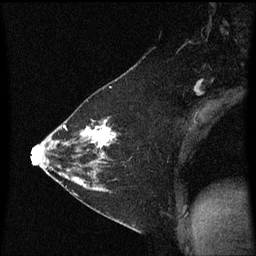
Breast MRI (dynamic contrast-enhanced), one sagittal slice; position 38 of 60 along the scan axis; dynamic contrast-enhanced series, image 2 of 3 at this slice position (ordered by acquisition); 1.5 T; TE 4.2 ms, TR 8.4 ms; 2 mm slice thickness; 256 × 256 image matrix, field of view 200 × 200 mm. Female patient, age 36 years. Case-level facts recorded for this patient, not image findings: setting: breast cancer imaged before/during neoadjuvant chemotherapy; receptor status: HR-positive, HER2-negative.
Outlined on this slice (semi-automatic segmentation, software-assisted and operator-edited):
- analysis volume of interest (the breast-tissue region the enhancement analysis was run in; not a lesion): bounding box <72,116,117,187> (left, top, right, bottom; pixels)
- tumour enhancement mask (voxels above the 70 % enhancement threshold inside the analysis volume of interest): <74,120,117,183>